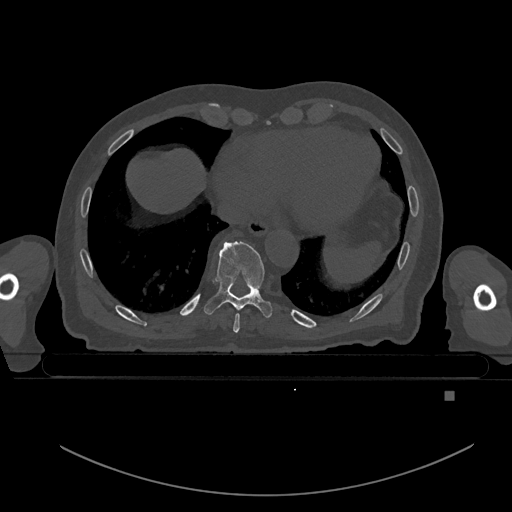
CT including the spine, one axial slice. Slice 152 of 969 in the series (ordered by position). Bone window (W 1800 / L 400 HU). 512 × 512 image matrix, field of view 456 × 456 mm. Male patient, age 82 years. Case-level facts recorded for this patient, not image findings: primary cancer: prostate; vertebrae with lytic lesions (as recorded): T11, T9, T8, T2.
Annotated regions visible in this slice (semi-automatic segmentation, software-assisted and operator-edited):
- T8 vertebra: bounding box <233,313,240,333> (left, top, right, bottom; pixels)
- T9 vertebra: <204,241,272,318>